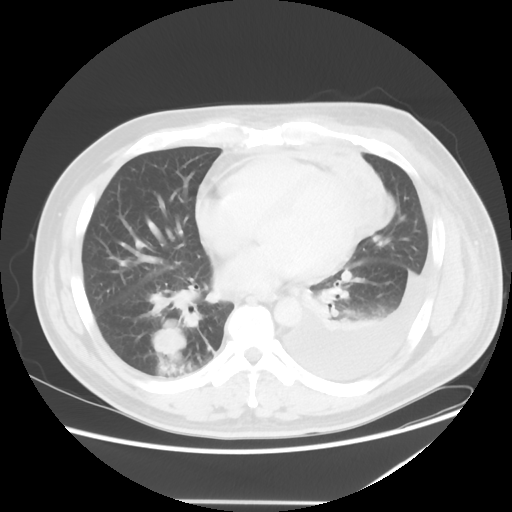
Chest CT, one axial slice. Position 20 of 52 along the scan axis. Reconstruction kernel STANDARD. Lung window (W 1500 / L -600 HU). 512 × 512 image matrix, field of view 405 × 405 mm. Patient: male, 42 years. From the clinical record (not read from this slice): clinical TNM (as recorded): T2 N1 M1.
Annotated regions visible in this slice (rectangle marked by the reading radiologist):
- lung tumour (recorded histology: adenocarcinoma): bounding box (x1, y1, x2, y2) in pixels: (149, 322, 202, 361)